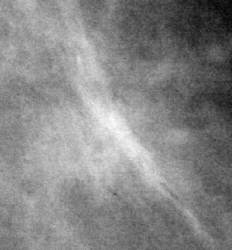
Crop from a digitized film mammogram around one marked abnormality; left breast; MLO view.
- Marked abnormality: mass, shape irregular, margins spiculated; BI-RADS assessment category 4; pathology result (as recorded, not read from the image): malignant.